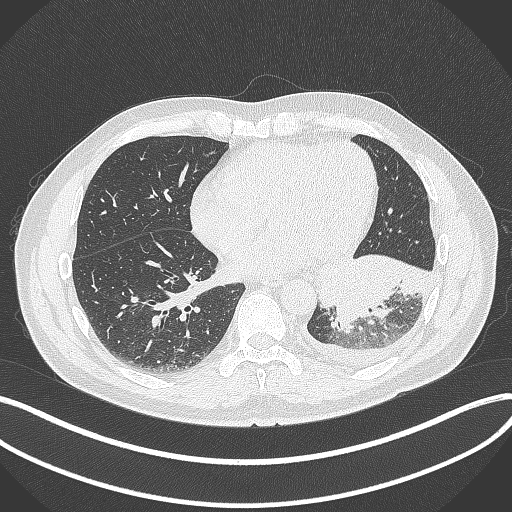
Chest CT, one axial slice. Position 129 of 342 along the scan axis. Reconstruction kernel B70f. 120 kVp. Lung window (W 1500 / L -600 HU). 512 × 512 image matrix, field of view 400 × 400 mm. Patient: male, 58 years. Case-level facts recorded for this patient, not image findings: clinical TNM (as recorded): T3 N1 M1b; histopathological grade: G3.
Outlined on this slice (bounding box drawn by a radiologist):
- lung tumour (recorded histology: small cell carcinoma): bounding box (x1, y1, x2, y2) in pixels: (315, 250, 435, 332)